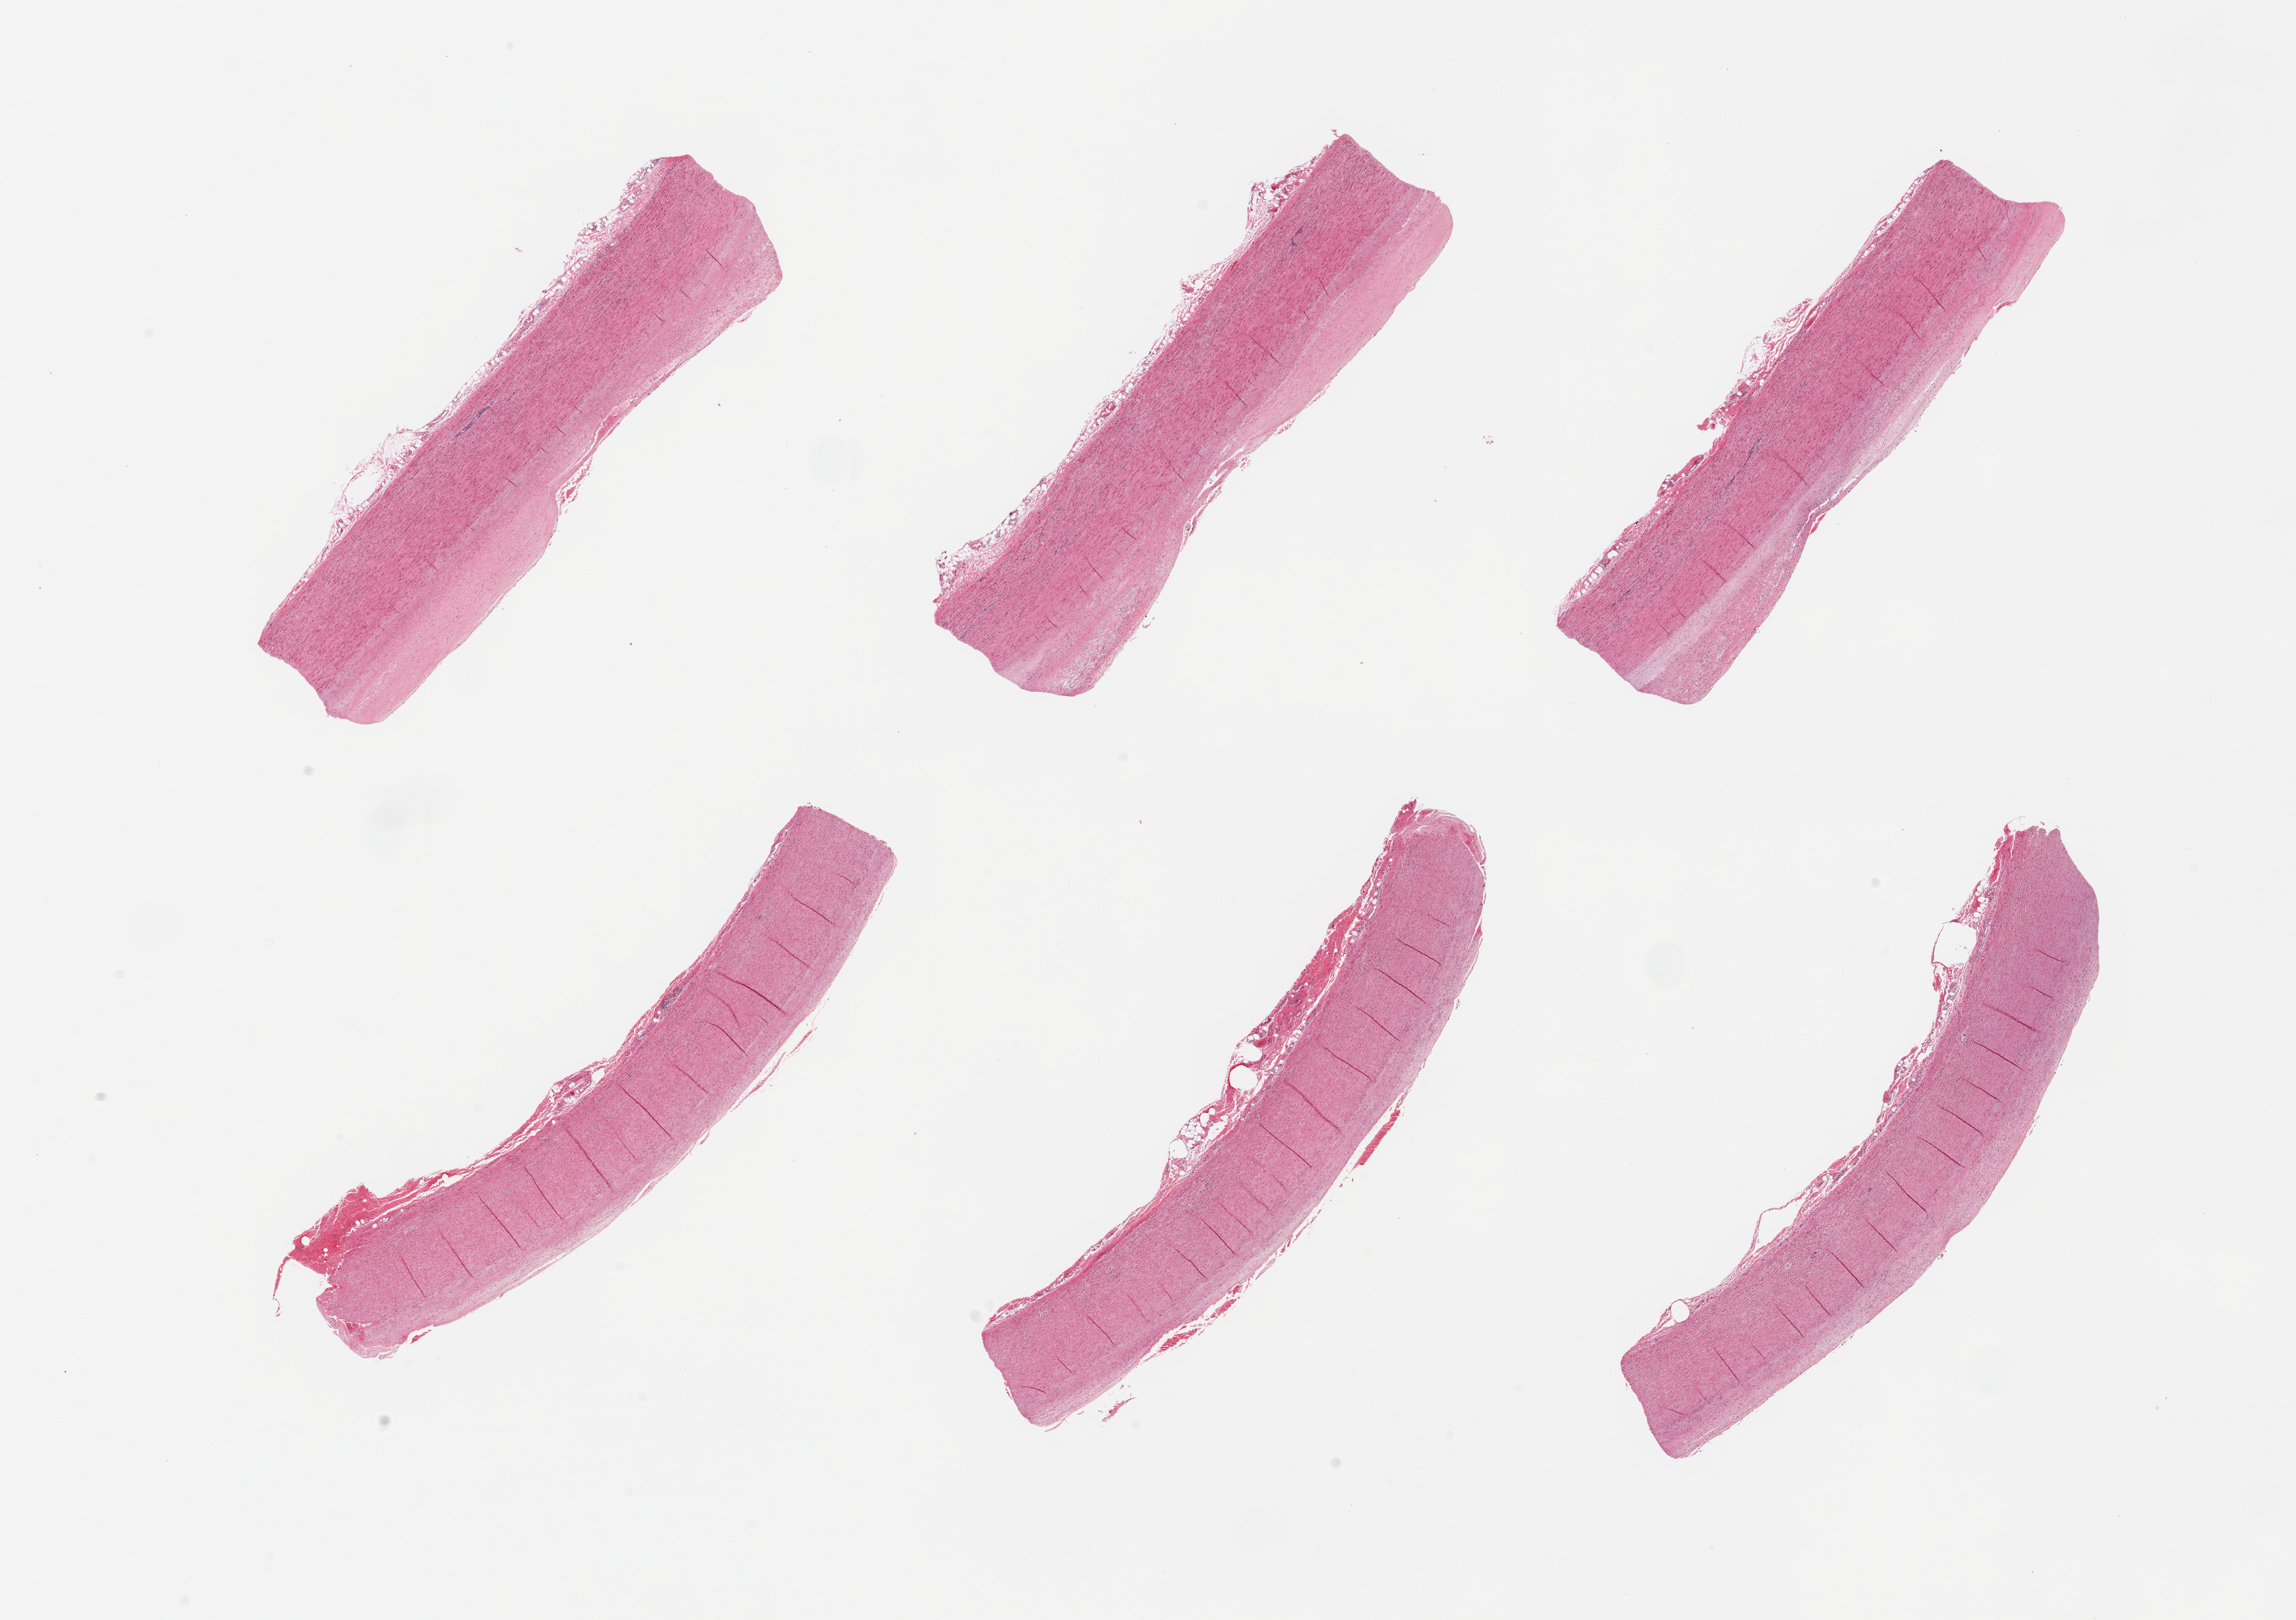
Whole-slide image, haematoxylin and eosin stain — whole scanned area (about 26.6 x 18.8 mm) shown as a low-resolution overview; PAXgene-fixed, paraffin-embedded tissue; target tissue: aorta; tissue donor sample. Donor sex: male.
Reviewer comment on this tissue sample: 6 pieces, atherosis up to ~0.8mm.